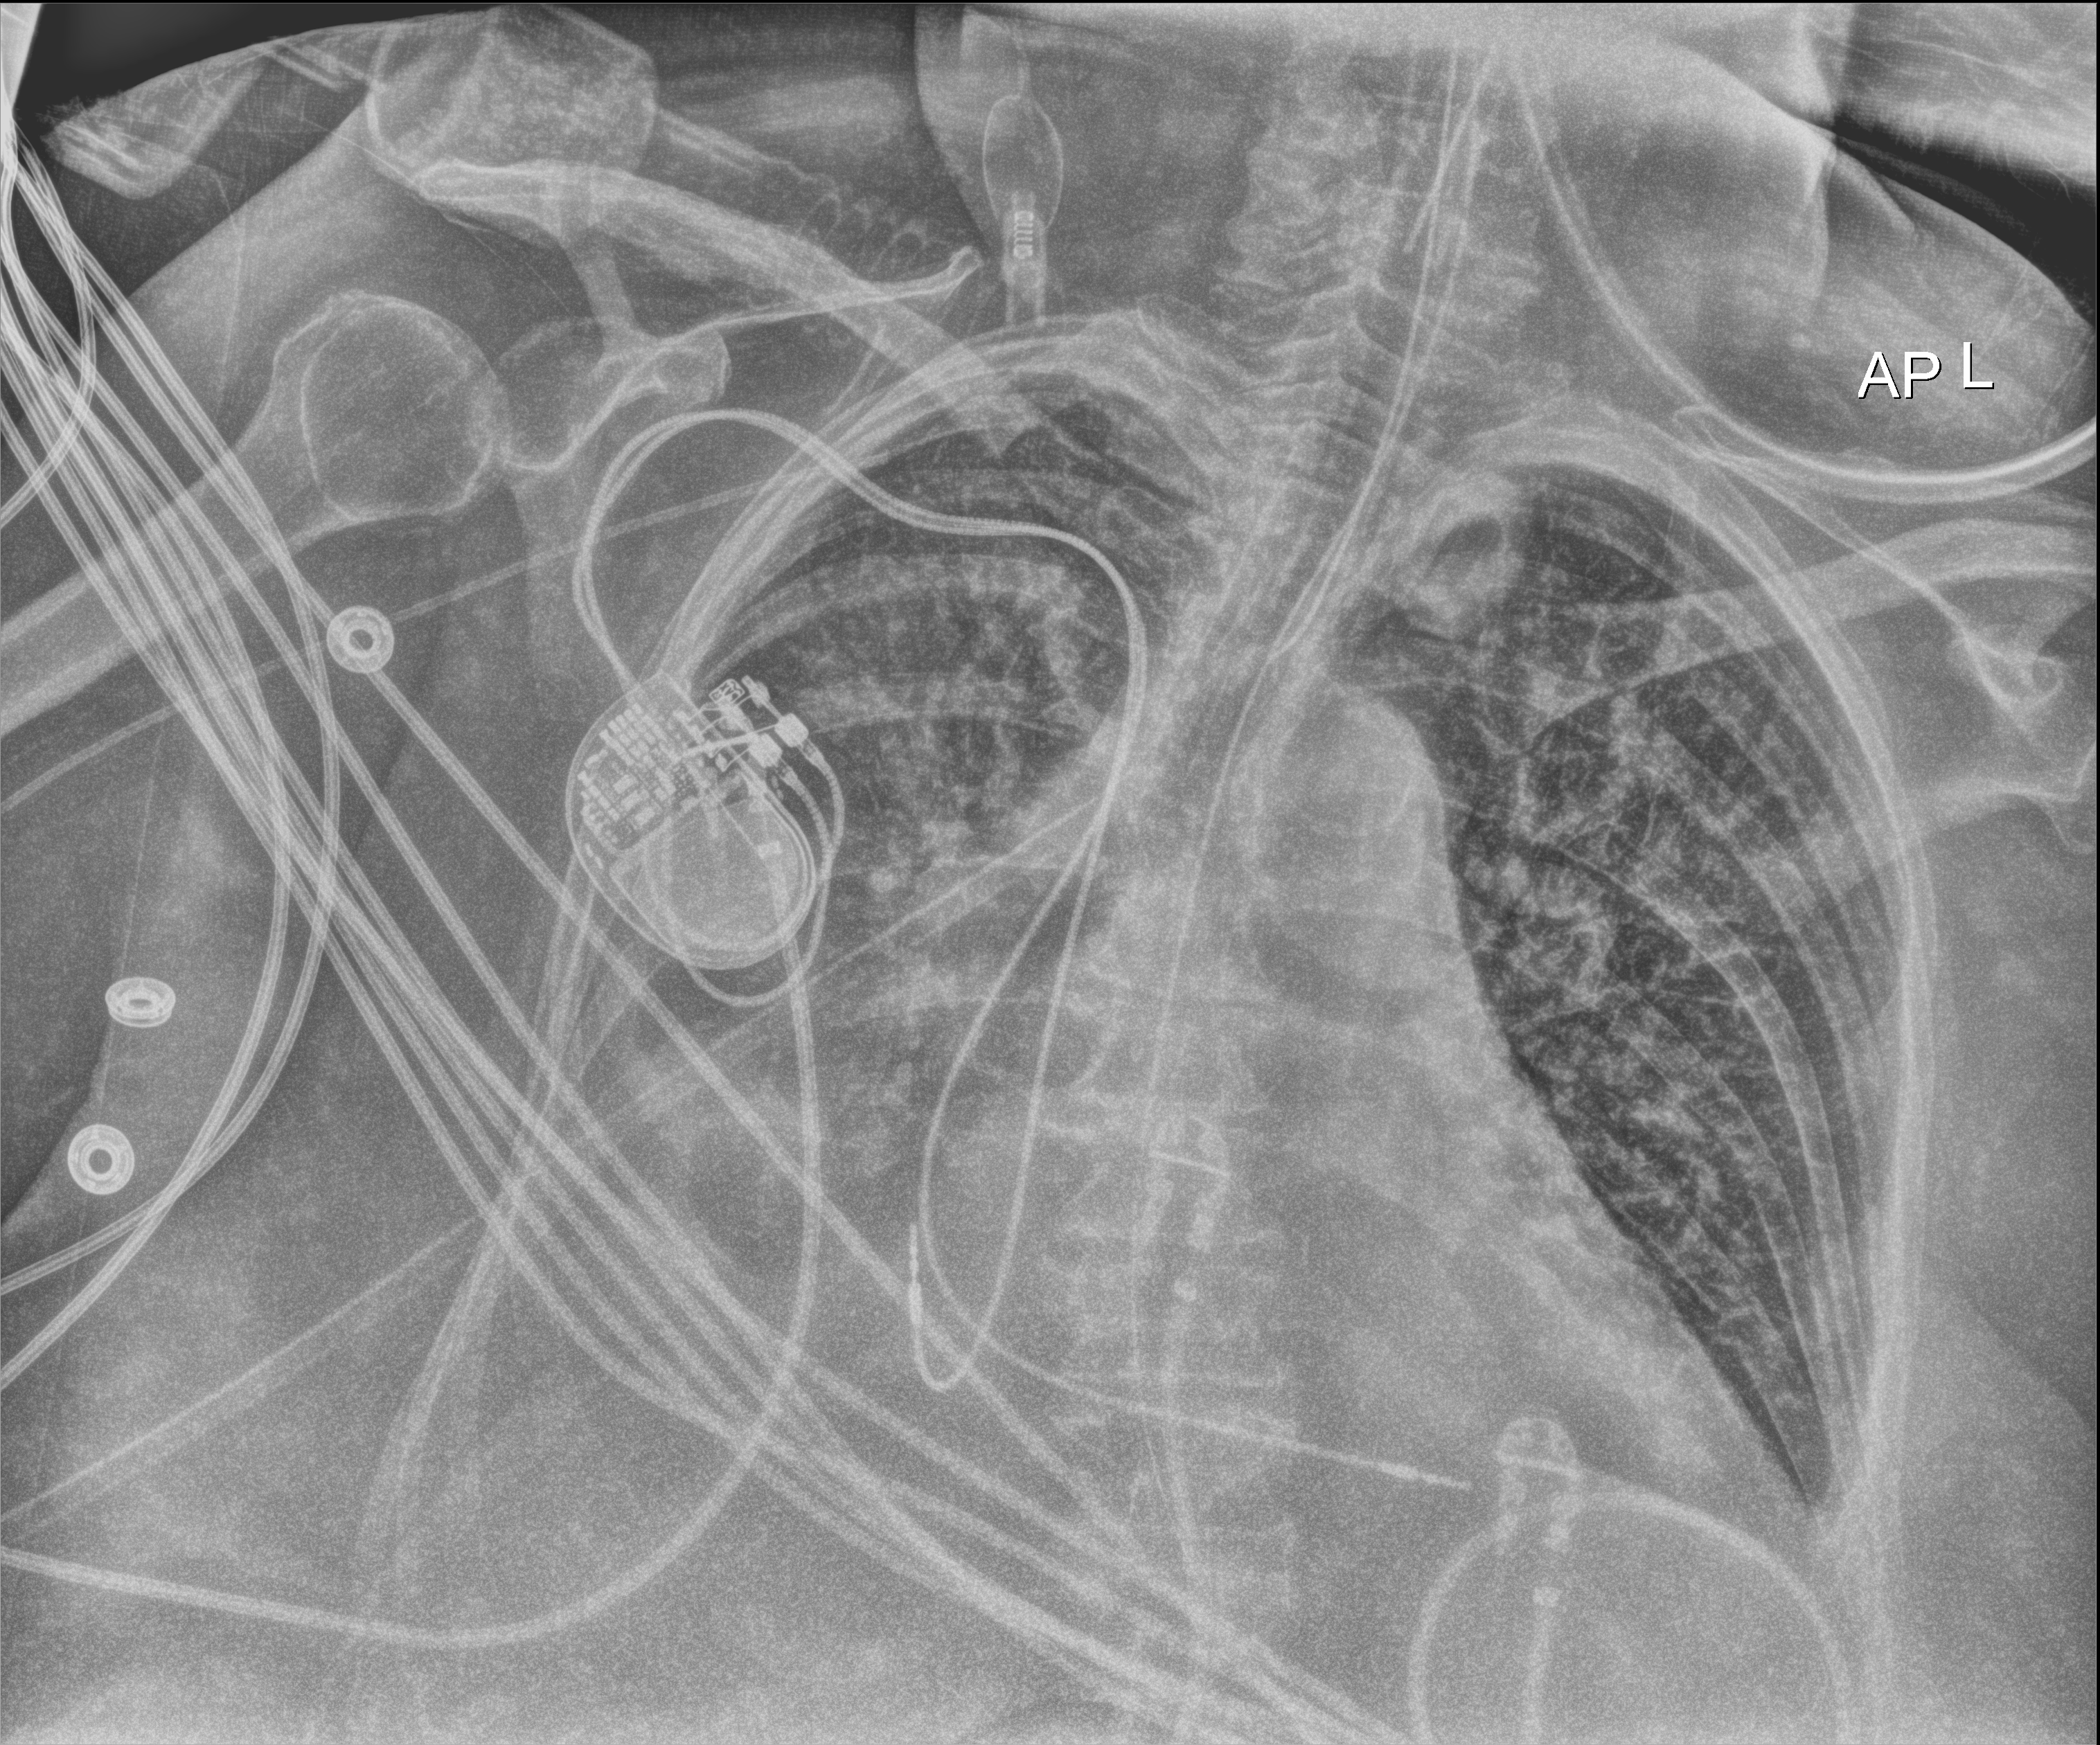
Bedside chest radiograph (digital radiography), anteroposterior (AP) projection. Female patient hospitalised with COVID-19, age 75–90 years.
Hospital-stay facts (about this admission, not read from this image; timing relative to this image not recorded): admitted to intensive care during this hospital stay: yes; length of hospital stay: 21 days; mechanically ventilated during this hospital stay: yes.